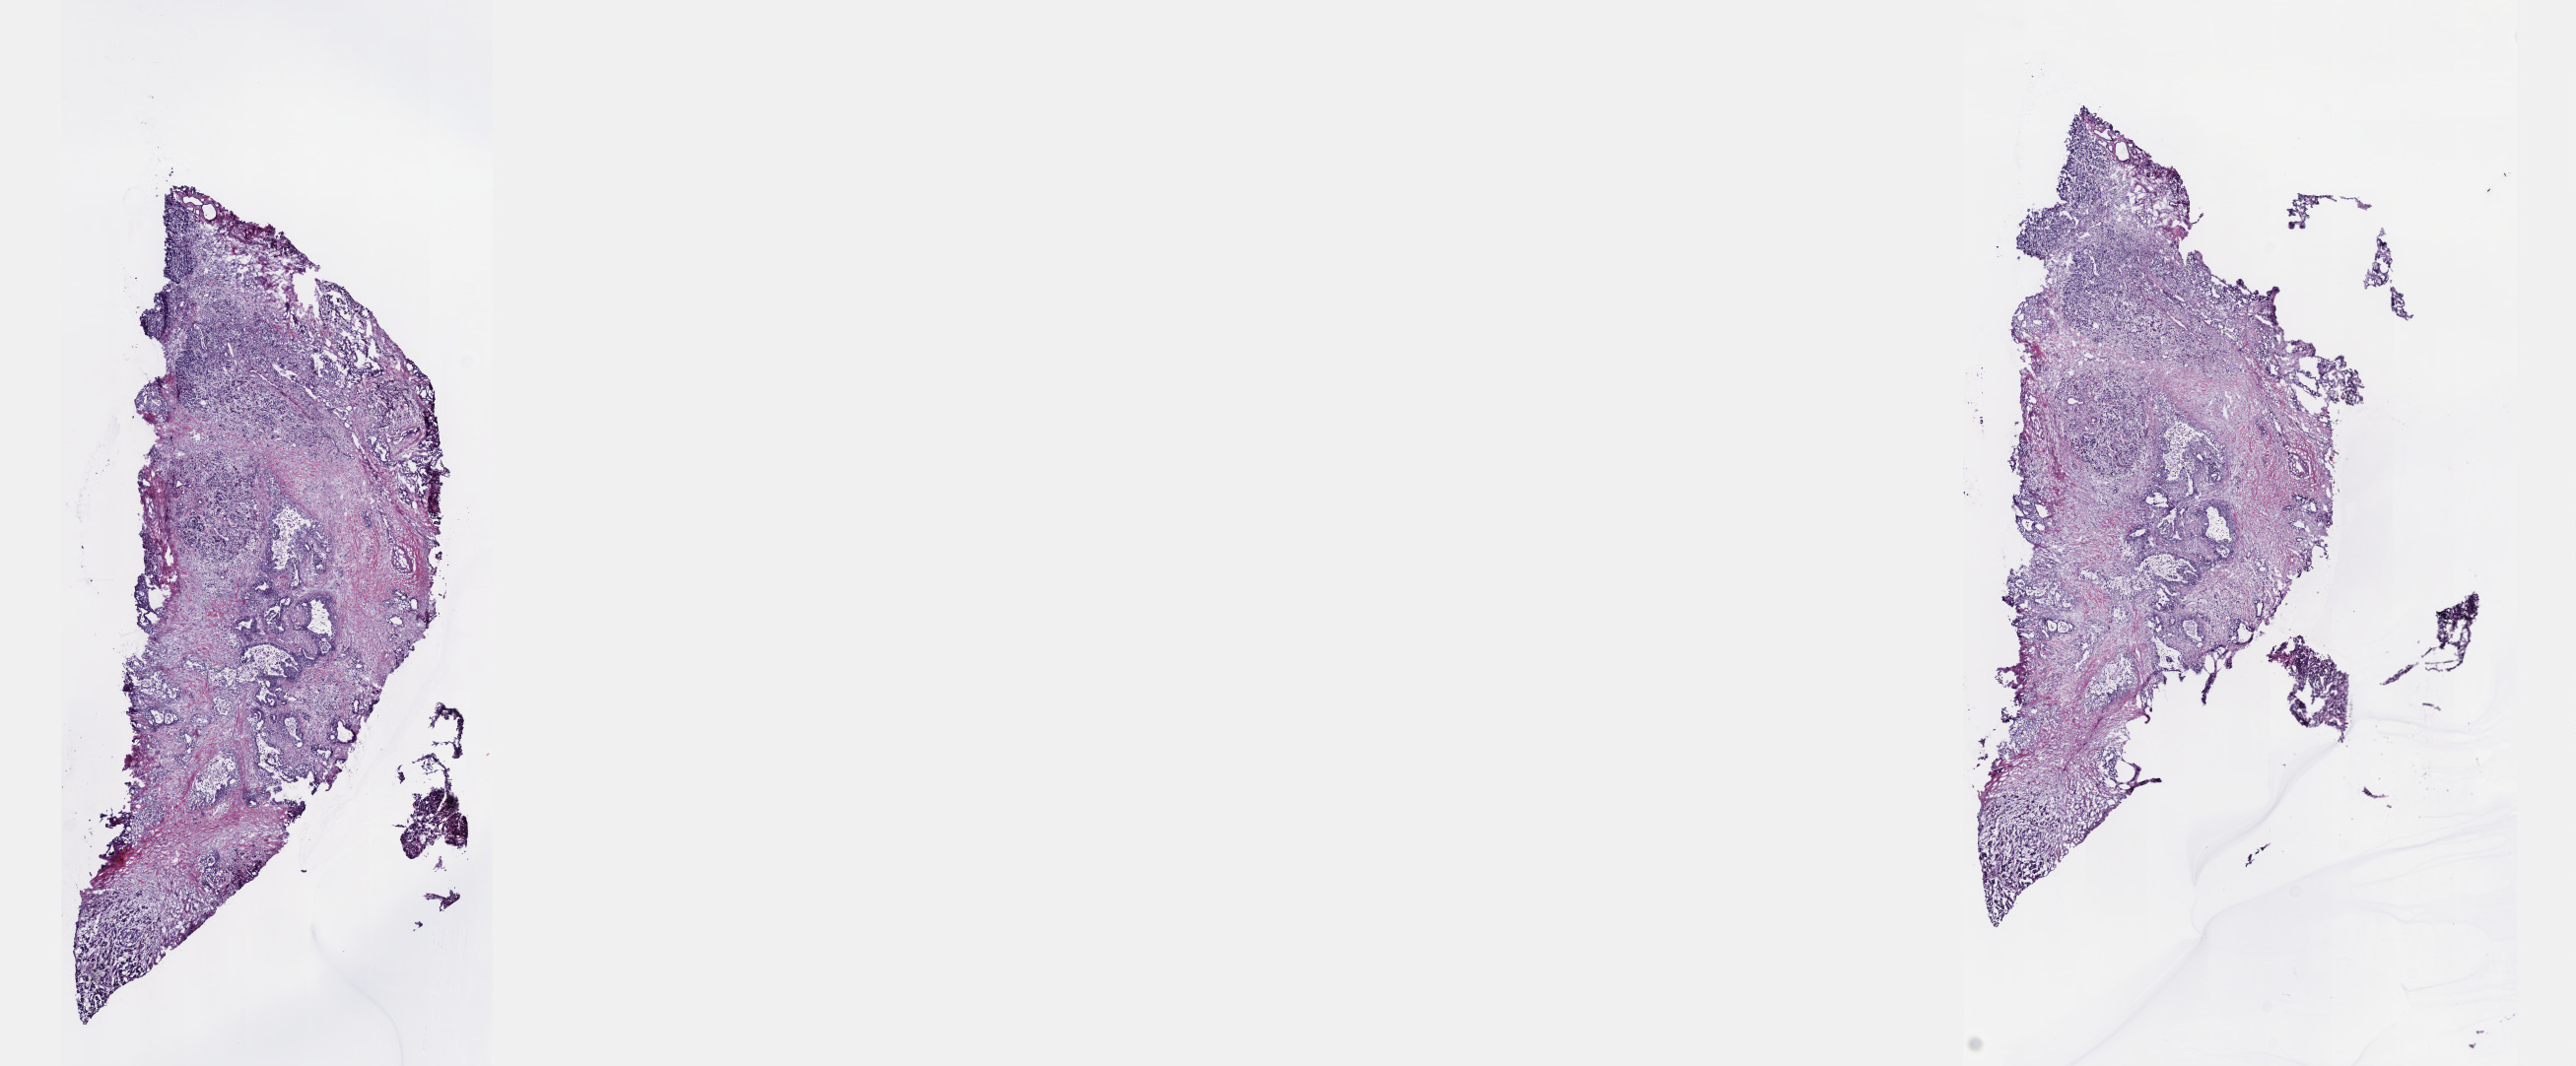
H&E-stained whole-slide image, whole scanned area (about 21.1 x 8.7 mm) shown as a low-resolution overview, frozen section, sample: primary tumour, pancreas. Patient: male, age at initial diagnosis 67 years. Histologic grade: G2 (moderately differentiated). Pathologist review of this section (percent, as recorded): tumour cells 70%, tumour nuclei 70%, normal cells 0%, stromal cells 30%, necrosis 0%. Infiltration values recorded for this section: lymphocyte infiltration 40%, monocyte infiltration 20%, neutrophil infiltration 20%.
• pathologic diagnosis: Infiltrating duct carcinoma, NOS
• AJCC pathologic stage: IIA
• lymph nodes positive (case pathology): 0 of 23 examined